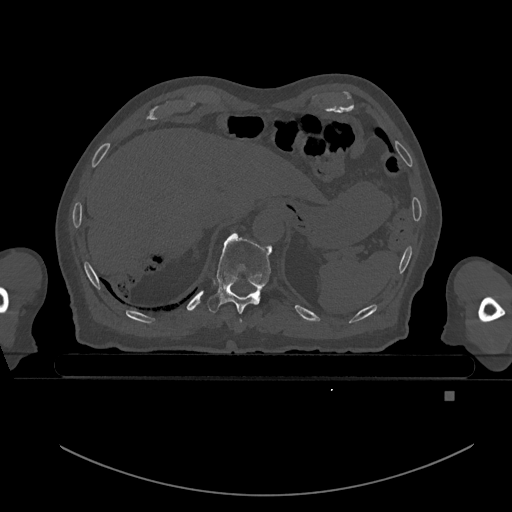
CT including the spine, one axial slice. Position 87 of 969 along the scan axis. Bone window (W 1800 / L 400 HU). 512 × 512 image matrix, field of view 456 × 456 mm. Male patient, age 82 years. Case-level facts recorded for this patient, not image findings: primary cancer: prostate; vertebrae with lytic lesions (as recorded): T11, T9, T8, T2.
Structures marked on this image (semi-automatic segmentation, software-assisted and operator-edited):
- T10 vertebra: bounding box [x1, y1, x2, y2] px = [207, 233, 272, 313]
- T9 vertebra: [239, 319, 241, 323]